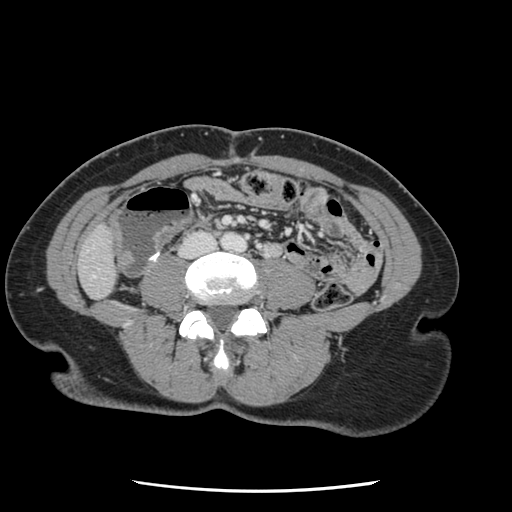
Contrast-enhanced abdominal CT, one axial slice; position 3 of 134 along the scan axis; 120 kVp; intravenous contrast given; soft-tissue window (W 400 / L 40 HU); 2.5 mm slice thickness; 512 × 512 image matrix. Female patient, age 43 years. Case-level facts recorded for this patient, not image findings: diagnosis: colorectal cancer liver metastases, imaged before liver resection; multiple liver metastases: yes; largest metastasis: 3.4 cm; disease in both lobes: yes.
Outlined on this slice (outlined manually by an expert reader):
- liver: bounding box <80,227,116,298> (left, top, right, bottom; pixels)
- planned liver remnant (the part of the liver to remain after resection): <80,228,116,299>